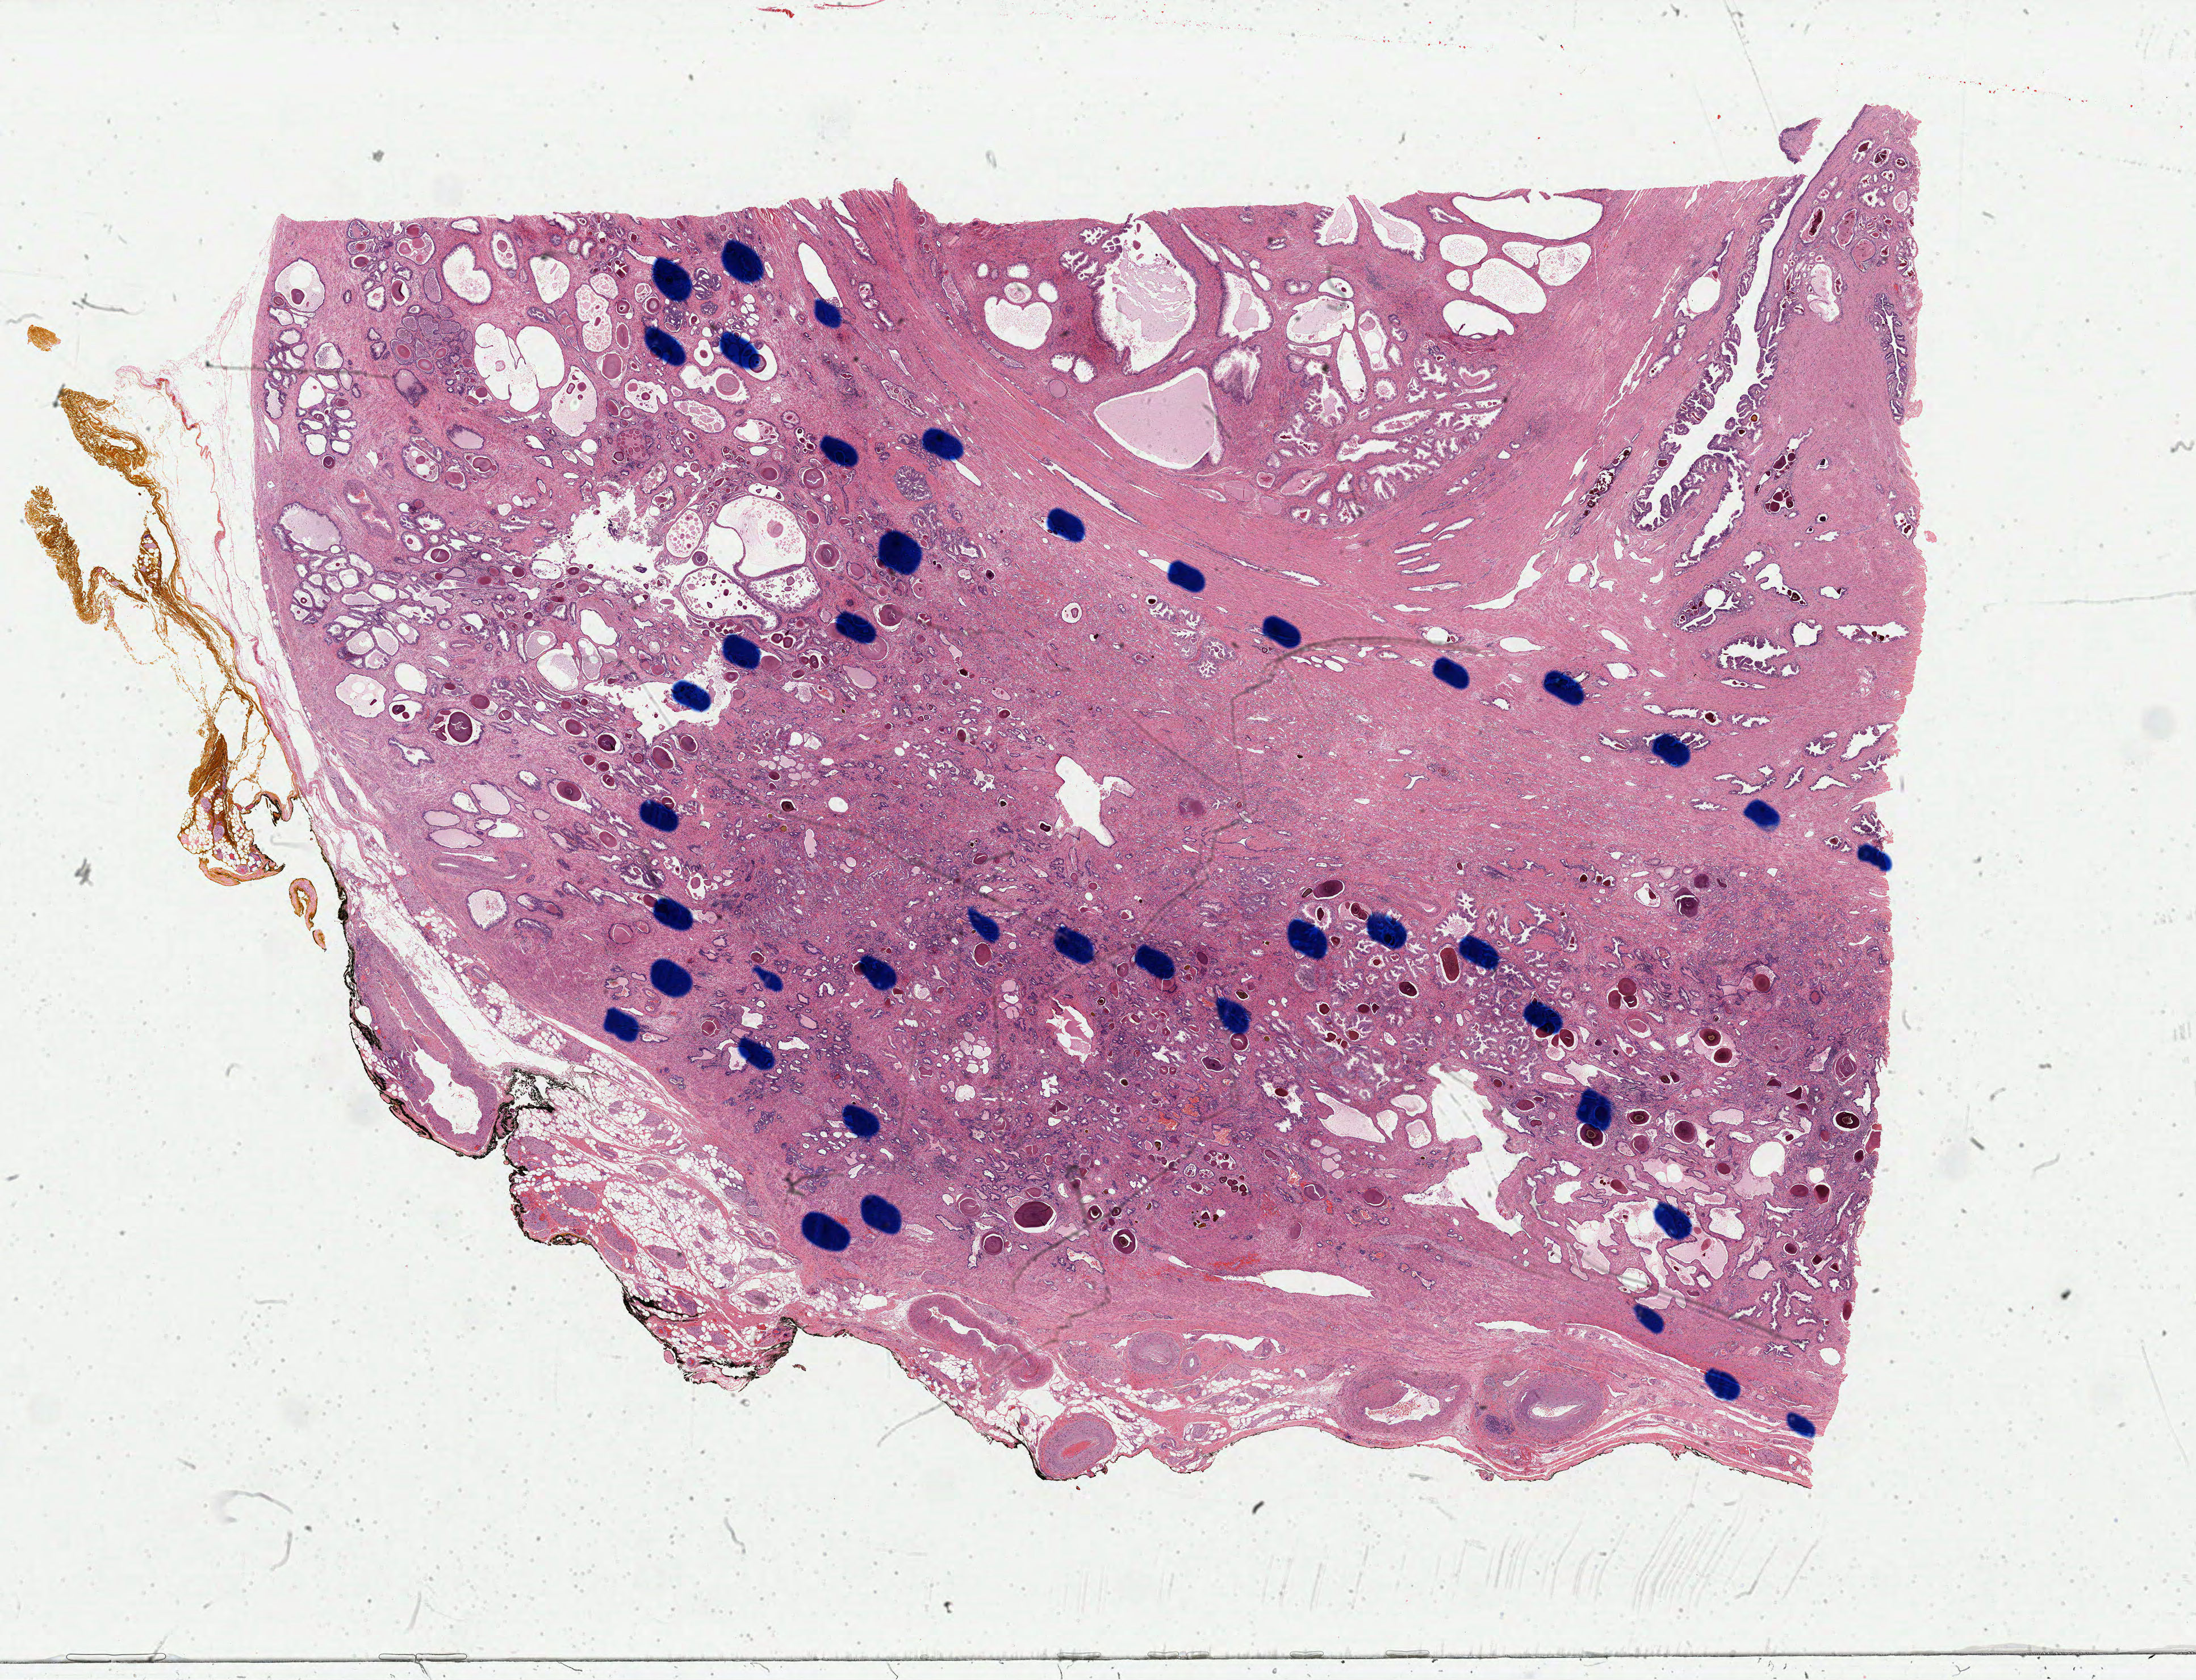
Hematoxylin and eosin (H&E) stained whole-slide image, shown as a low-resolution overview of the whole scanned area (about 30.5 x 23.4 mm). Formalin-fixed paraffin-embedded (FFPE) diagnostic section. Sample: primary tumour, prostate. Male patient; age at initial diagnosis 50 years. Gleason score: 7 (3+4).
- pathologic diagnosis: Adenocarcinoma, NOS (prostate gland)